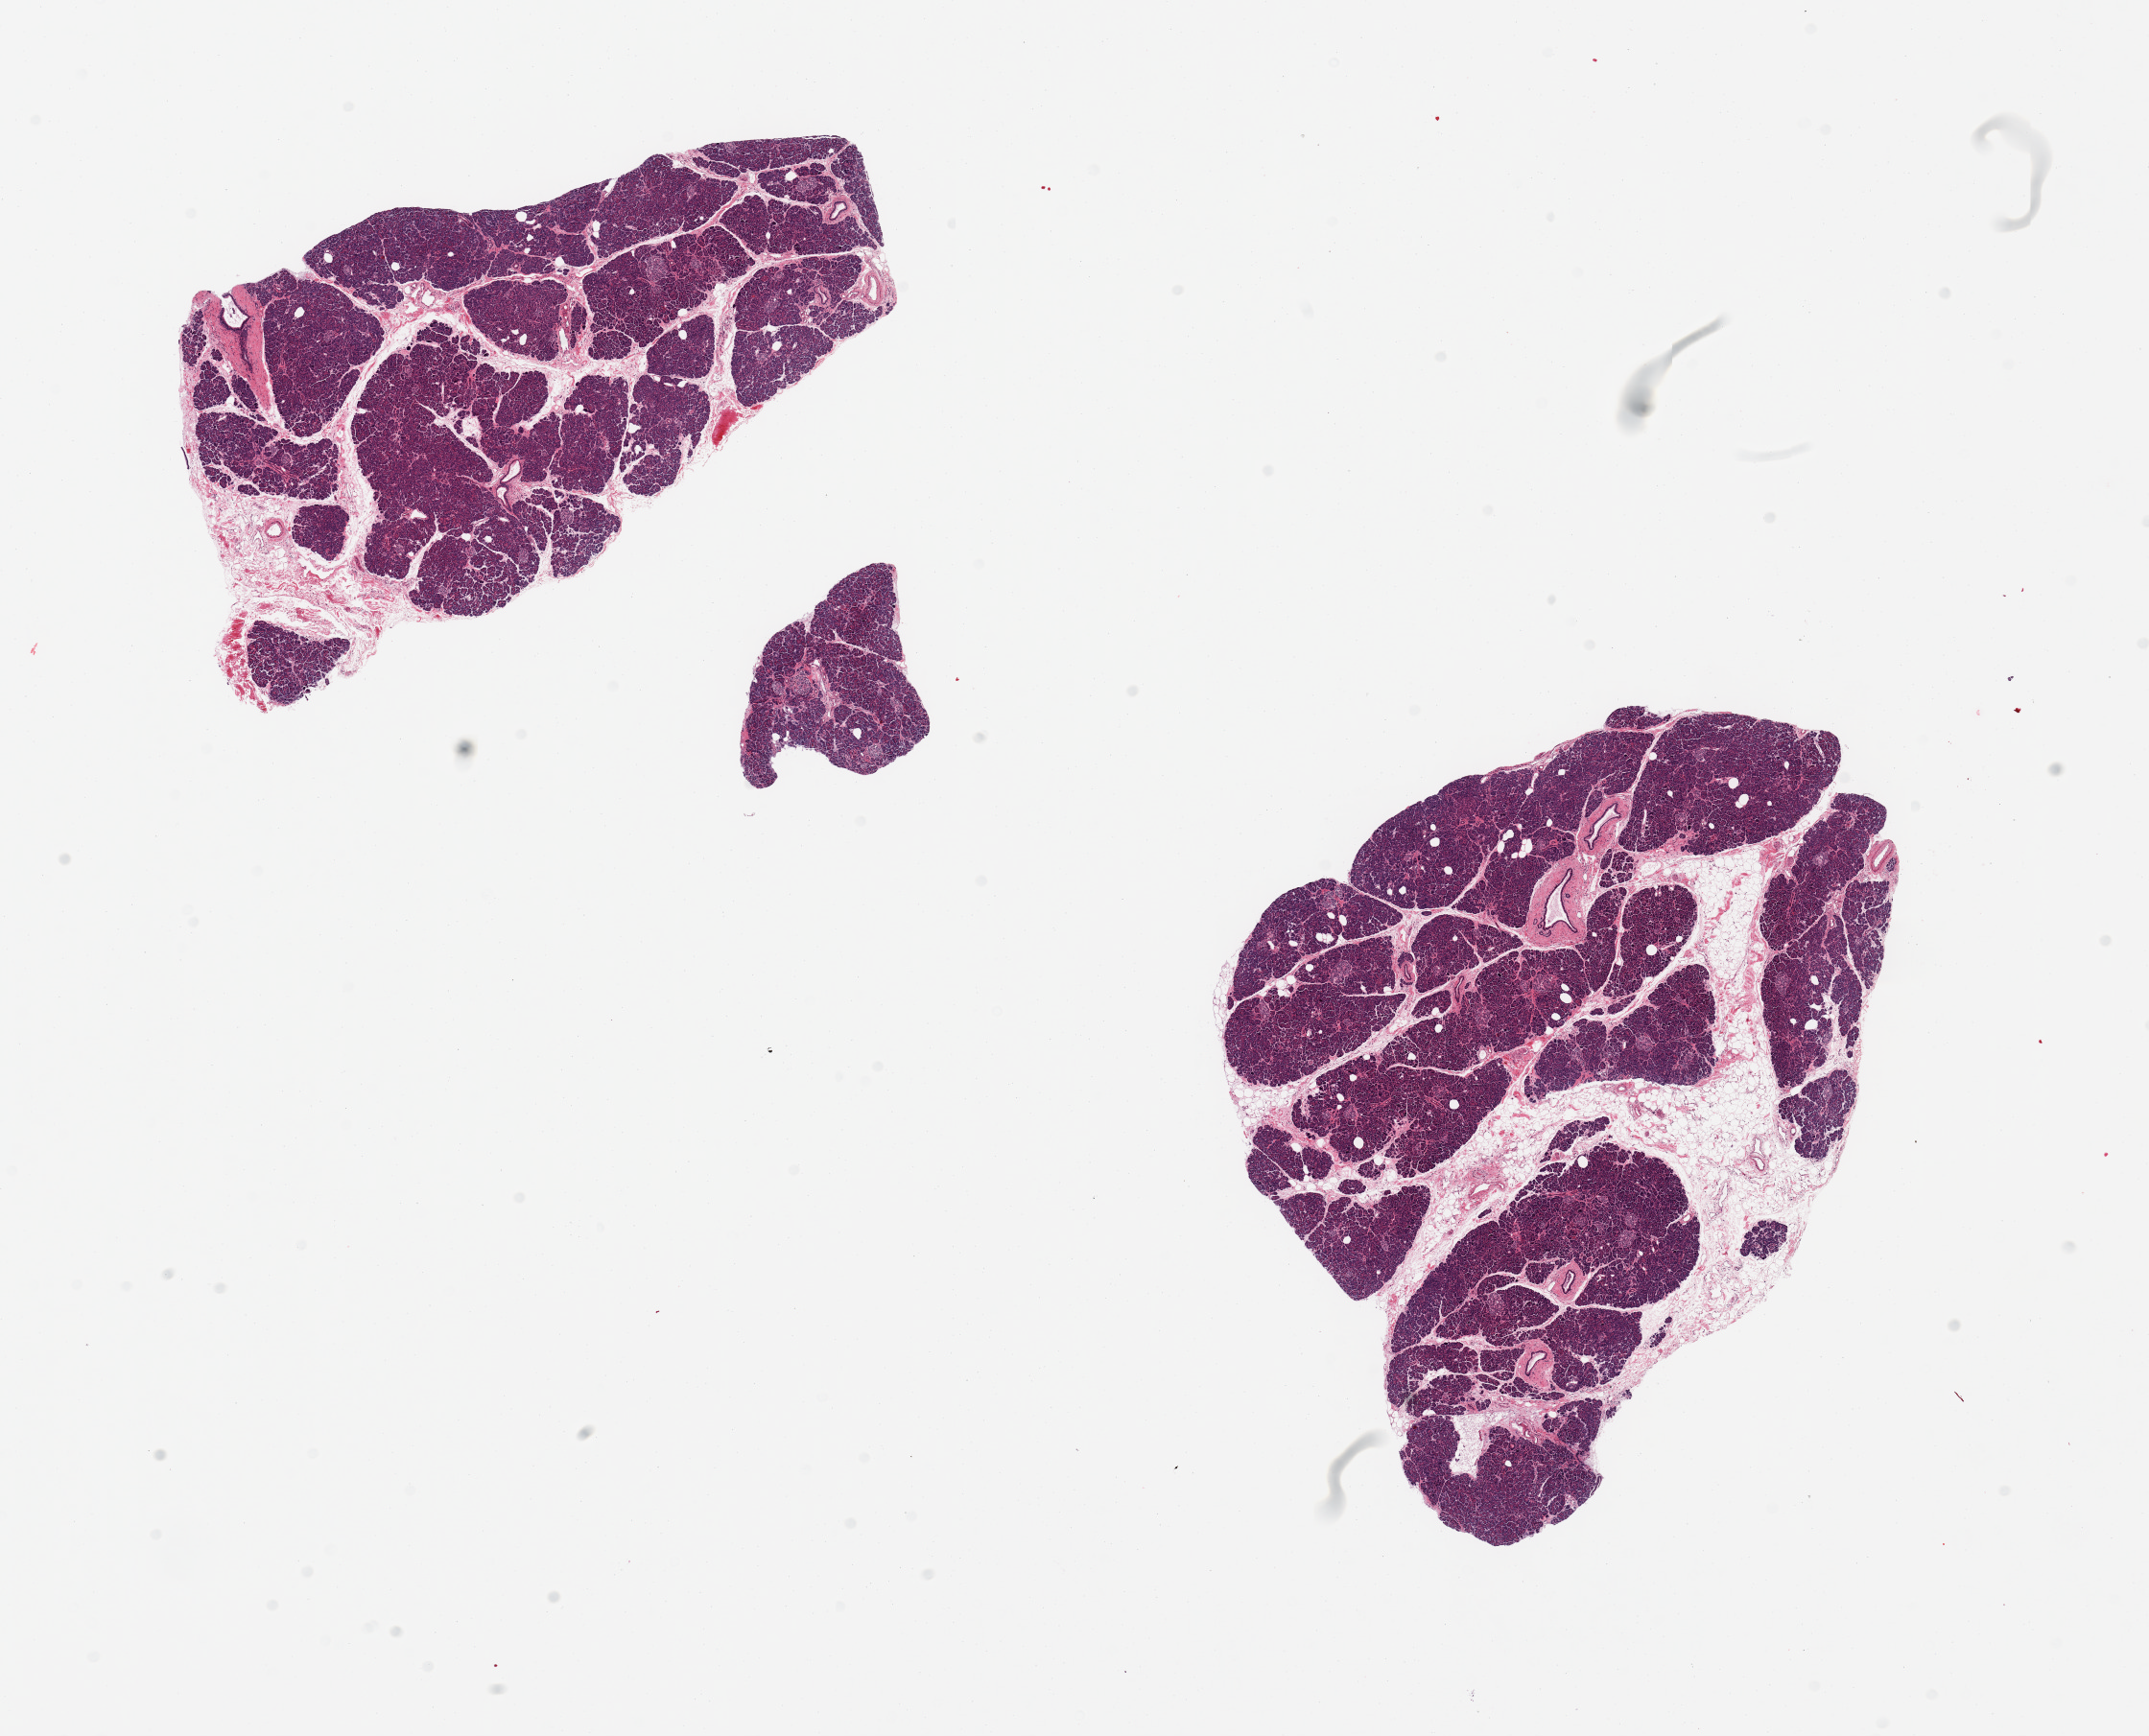
Hematoxylin and eosin (H&E) whole-slide image — low-resolution overview of the scanned area, about 17.7 x 14.3 mm; PAXgene-fixed paraffin-embedded (PFPE) section; section of pancreas (target tissue); tissue donor sample. Donor sex: female.
• reviewer comment on this tissue sample: 2 pieces; 10 & 20% internal fat